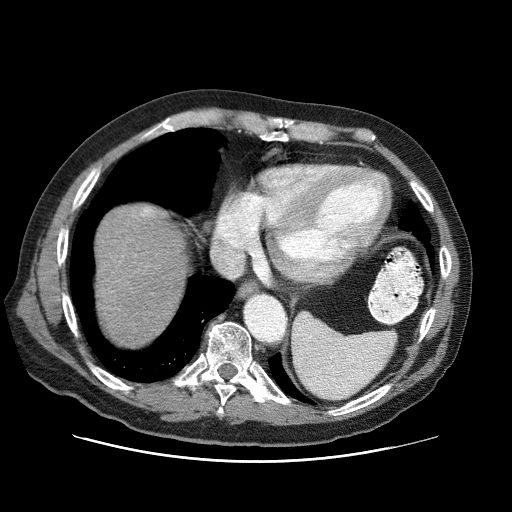
Contrast-enhanced abdominal CT (liver protocol), one axial slice. Position 69 of 87 along the scan axis. Reconstruction kernel STANDARD. 120 kVp. One of 3 acquisitions stored at this slice position. Soft-tissue window (W 400 / L 40 HU). 2.5 mm slice thickness. 512 × 512 image matrix. From the clinical record (not read from this slice): diagnosis: hepatocellular carcinoma (patient treated with transarterial chemoembolisation; whether this scan precedes or follows treatment is not stated here); TNM stage (as recorded): Stage-IIIA; Child-Pugh class: A; tumour differentiation: well differentiated; tumour nodularity: multinodular.
Structures marked on this image (semi-automatic segmentation, software-assisted and operator-edited):
- liver parenchyma outside the tumour (the mass and vessels are separate outlines, so this box may not span the whole liver): bounding box <96,204,188,344> (left, top, right, bottom; pixels)
- liver vessels: <142,210,151,216>